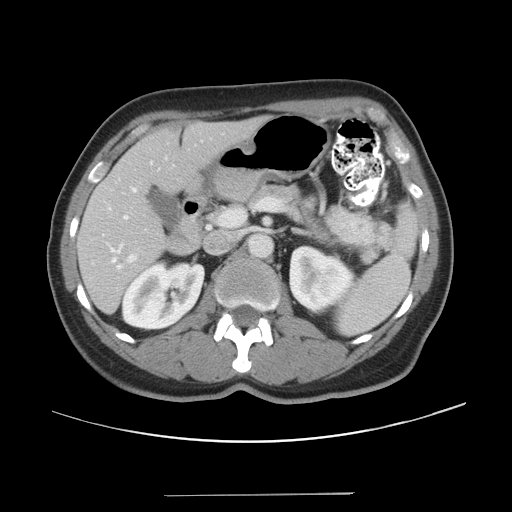
Contrast-enhanced abdominal CT, one axial slice. Position 20 of 43 along the scan axis. Reconstruction kernel STANDARD. Soft-tissue window (W 400 / L 40 HU). 5 mm slice thickness. 512 × 512 image matrix, field of view 409 × 409 mm. Male patient, age 65 years. Case-level facts recorded for this patient, not image findings: diagnosis: colorectal cancer liver metastases, imaged before liver resection; multiple liver metastases: no; largest metastasis: 3.8 cm; disease in both lobes: no.
Structures marked on this image (expert manual segmentation):
- hepatic veins: bounding box <103,182,138,262> (left, top, right, bottom; pixels)
- liver: <79,121,255,312>
- planned liver remnant (the part of the liver to remain after resection): <79,121,254,312>
- portal vein (with intrahepatic branches): <103,161,153,264>